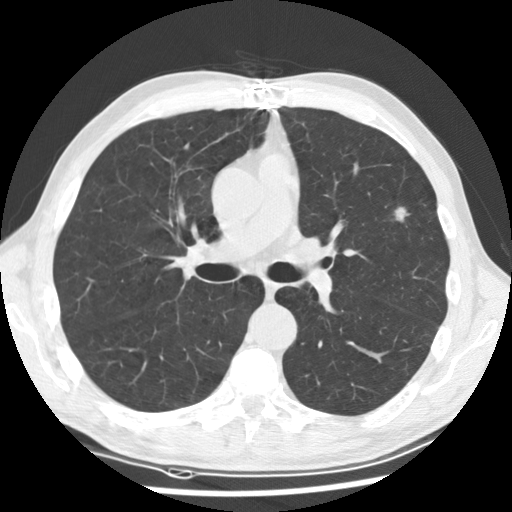
Axial slice from a low-dose chest CT screening exam. Baseline screening round. Lung window (W 1500 / L -600 HU). 2.5 mm slice thickness. Standard (soft-tissue) reconstruction kernel (STANDARD). 120 kVp. 512 × 512 image matrix, field of view 340 × 340 mm. Male, age 64 years at enrolment.
Lesion marked by an expert reader, bounding box <377,197,430,239> (left, top, right, bottom; pixels). Reader record for this screening exam (exam-level; its link to the box is not recorded): non-calcified nodule or mass ≥4 mm, left upper lobe, 13 × 10 mm, spiculated (stellate) margins, soft tissue attenuation. Participant outcome: lung cancer diagnosed 410 days after this screen (after the second annual screen) — adenocarcinoma, NOS, left upper lobe, poorly differentiated (G3), stage IA (AJCC 6th edition), 10 mm at pathology.